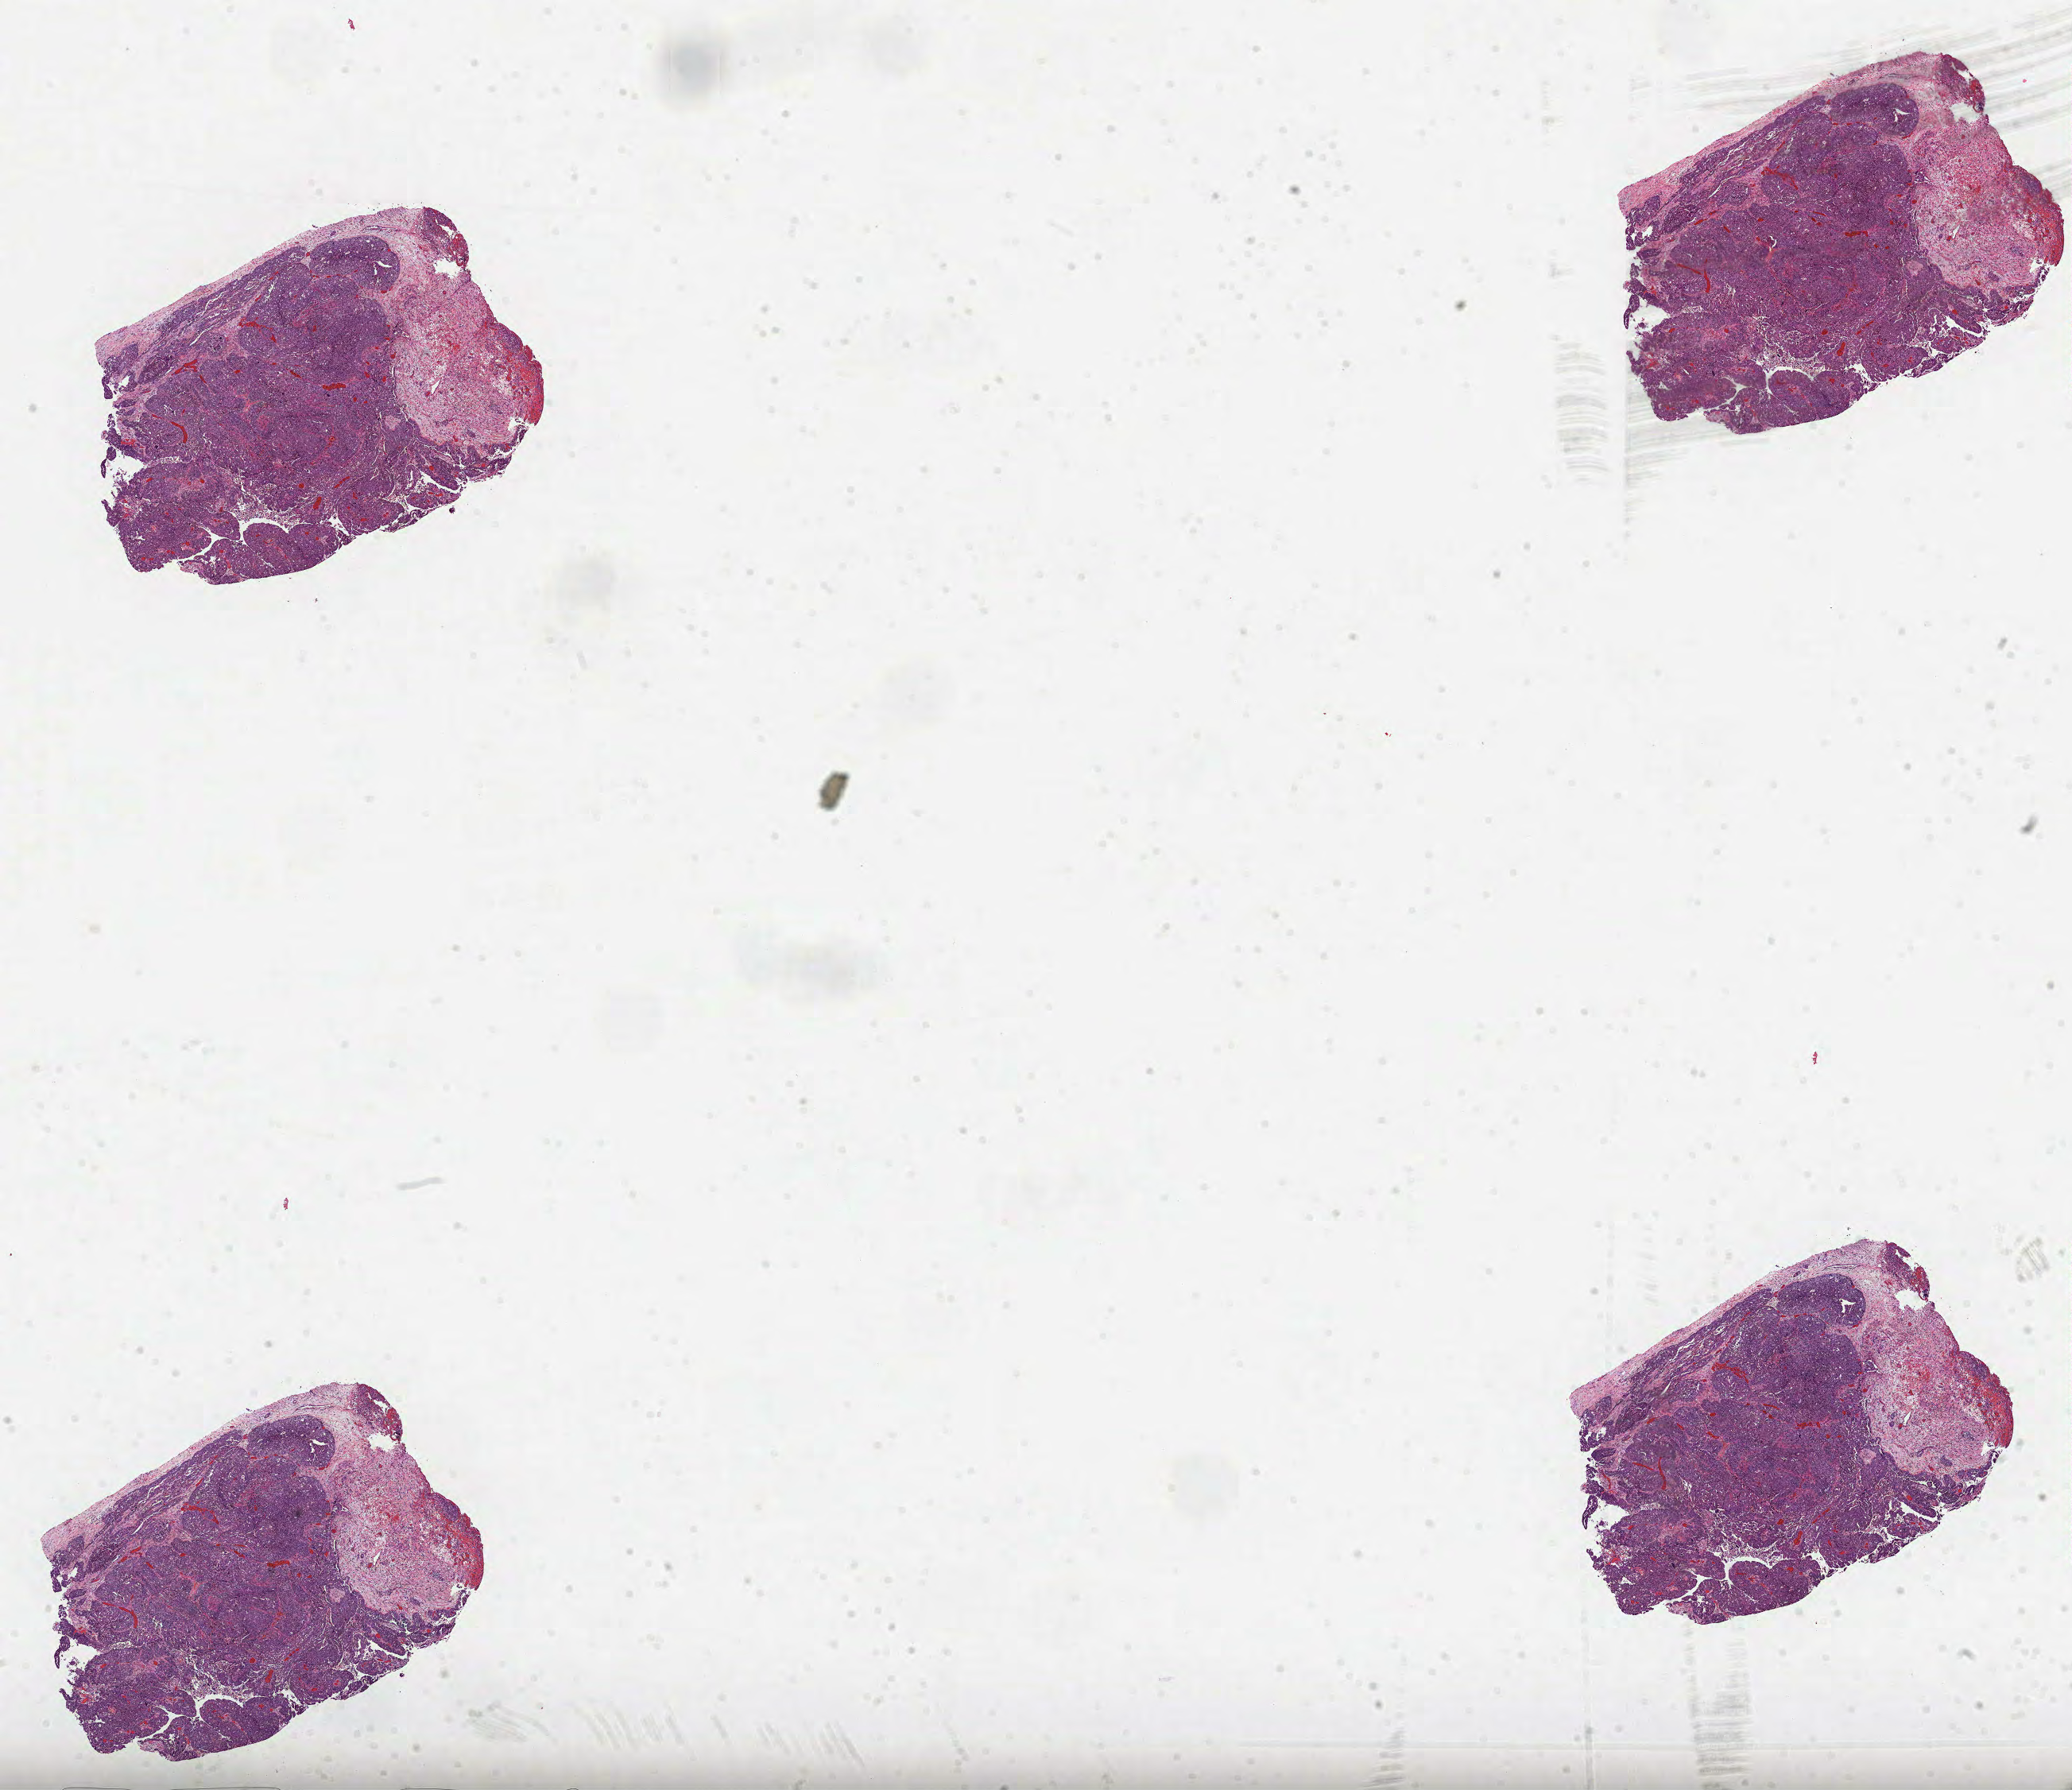
H&E whole-slide image, low-resolution overview of the scanned area, about 21.0 x 18.2 mm (from a 40x scan); formalin-fixed paraffin-embedded (FFPE) diagnostic section; primary tumour sample from the ovary. Female, age 54 years at initial diagnosis. Histologic grade: G3 (poorly differentiated).
FIGO stage: IIIC. Pathologic diagnosis: Serous cystadenocarcinoma, NOS.